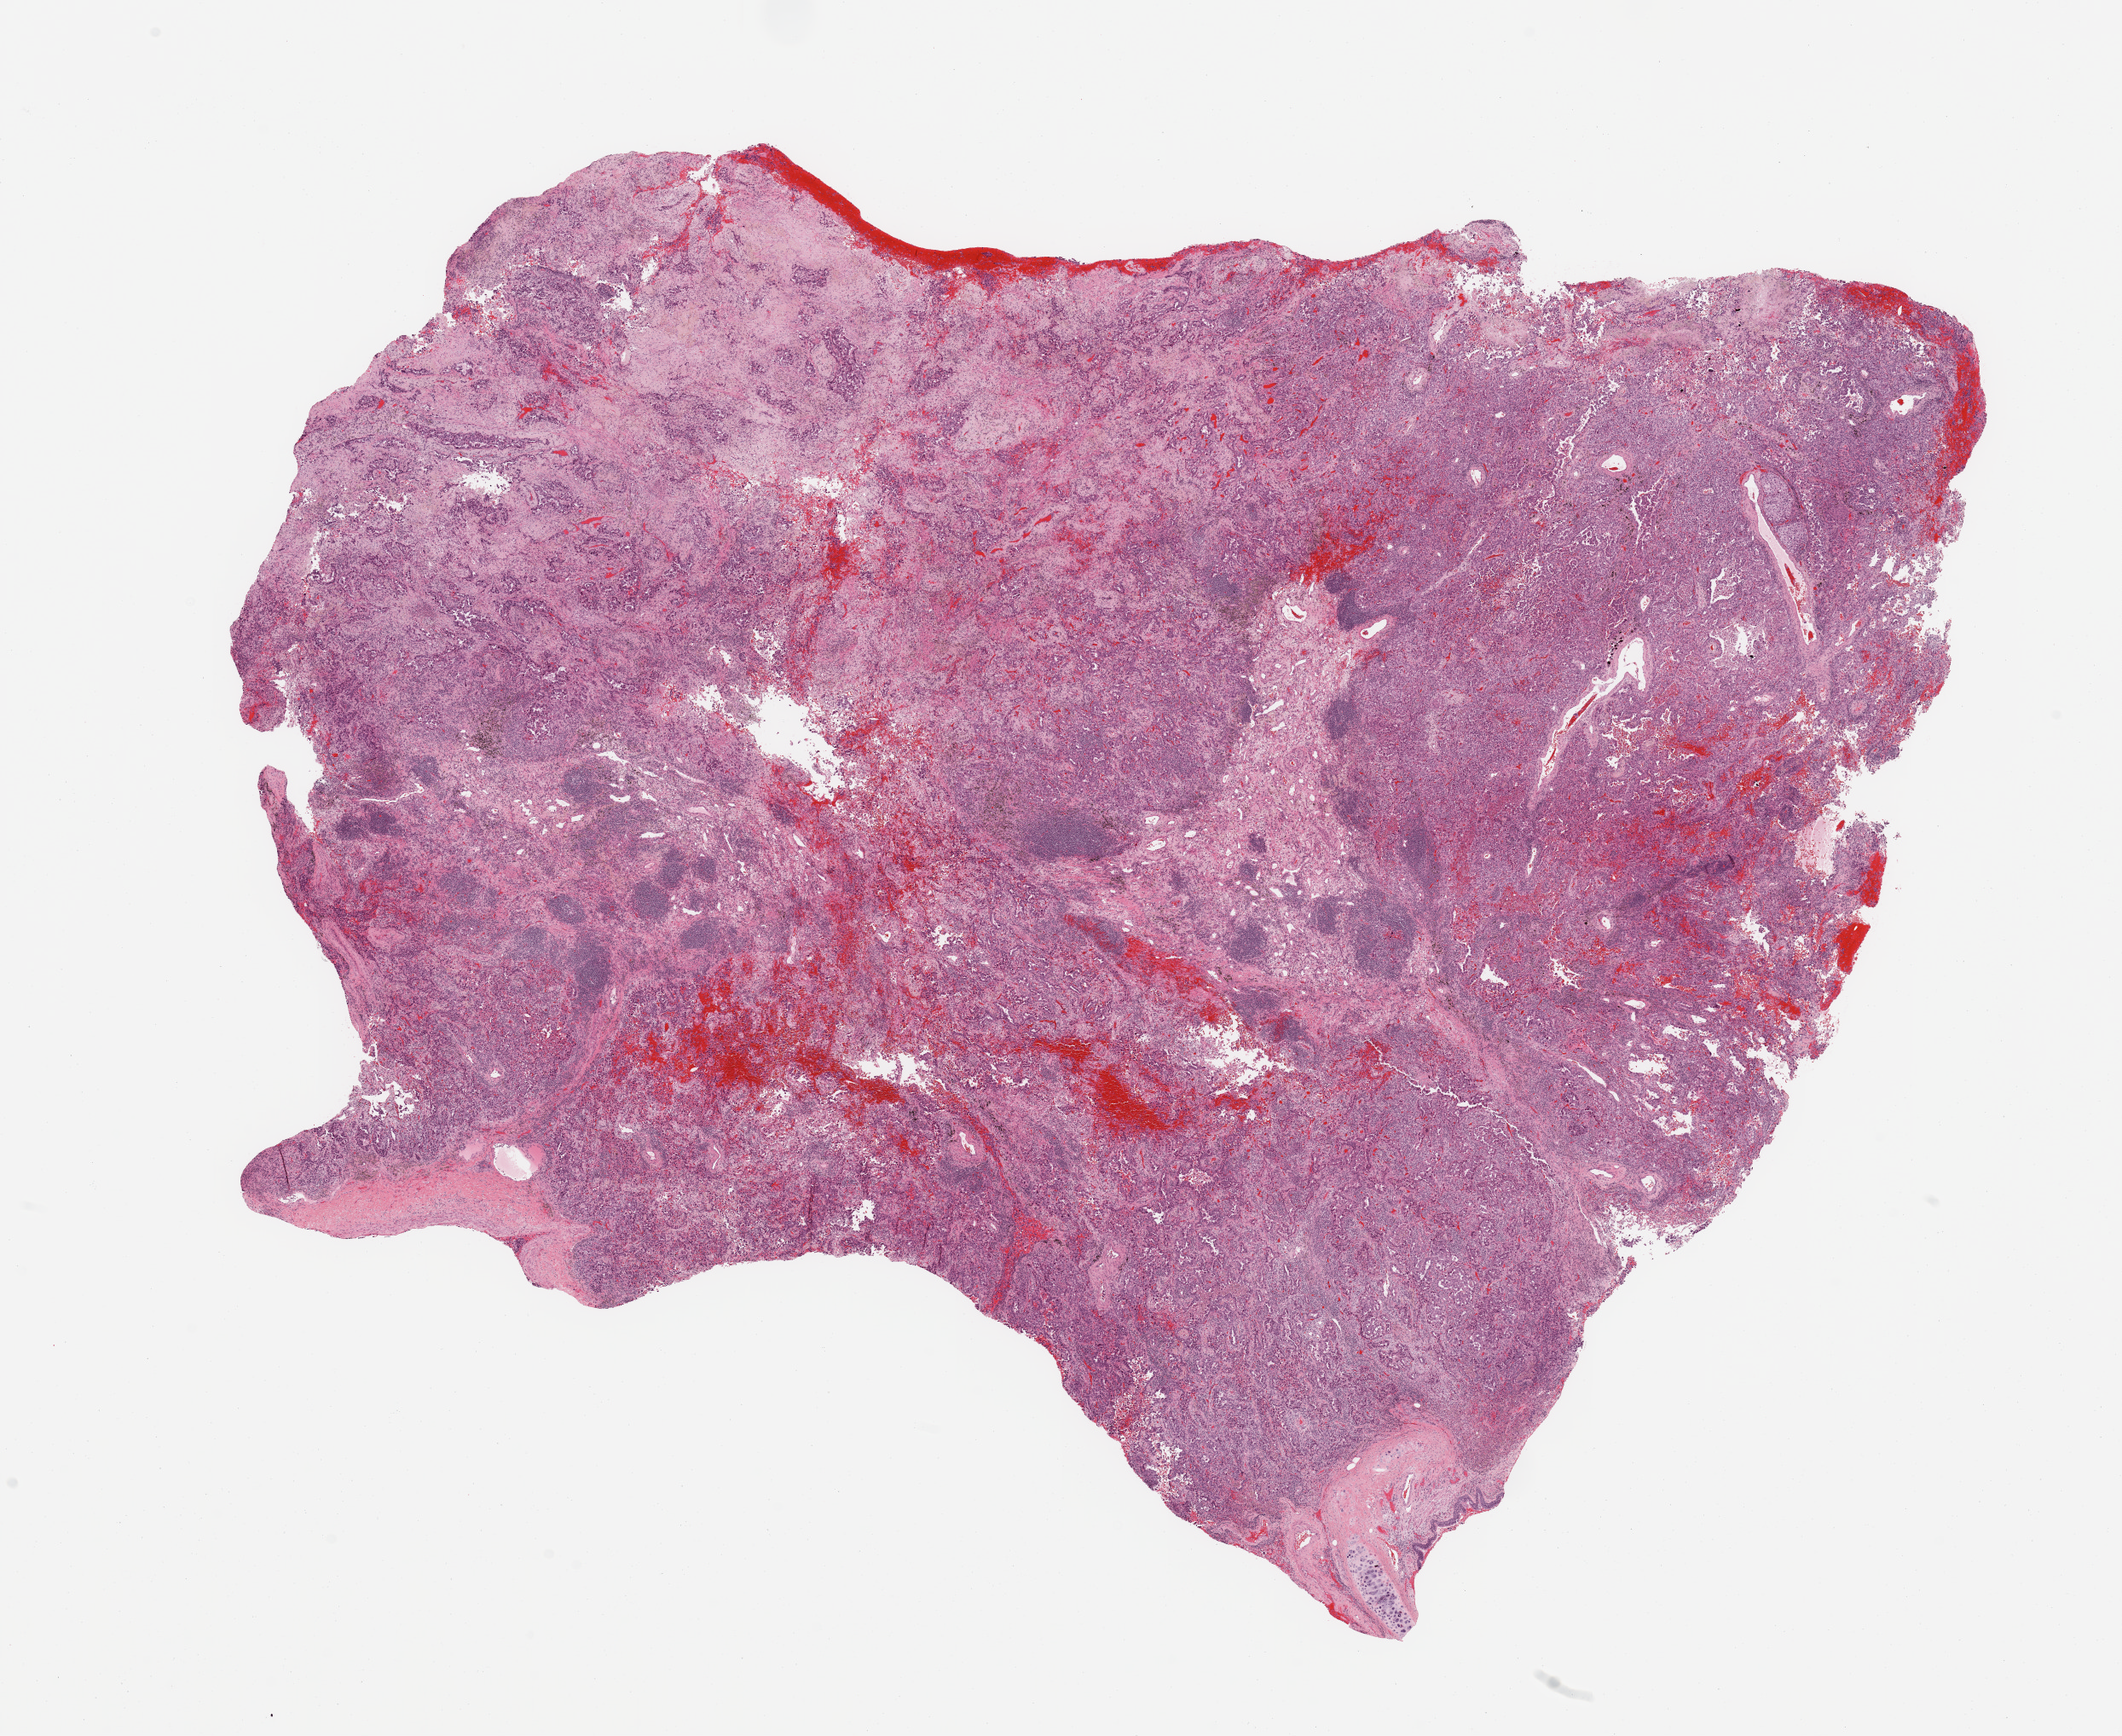
Digitized H&E tissue section (whole slide), a low-resolution overview of the entire scanned area, about 19.7 x 16.1 mm, lung, tumour tissue. 56-year-old female patient. Histologic grade: G2 (moderately differentiated).
AJCC pathologic stage: IIB. Histologic diagnosis: Adenocarcinoma, NOS. Primary tumour site (as recorded): left upper lobe.